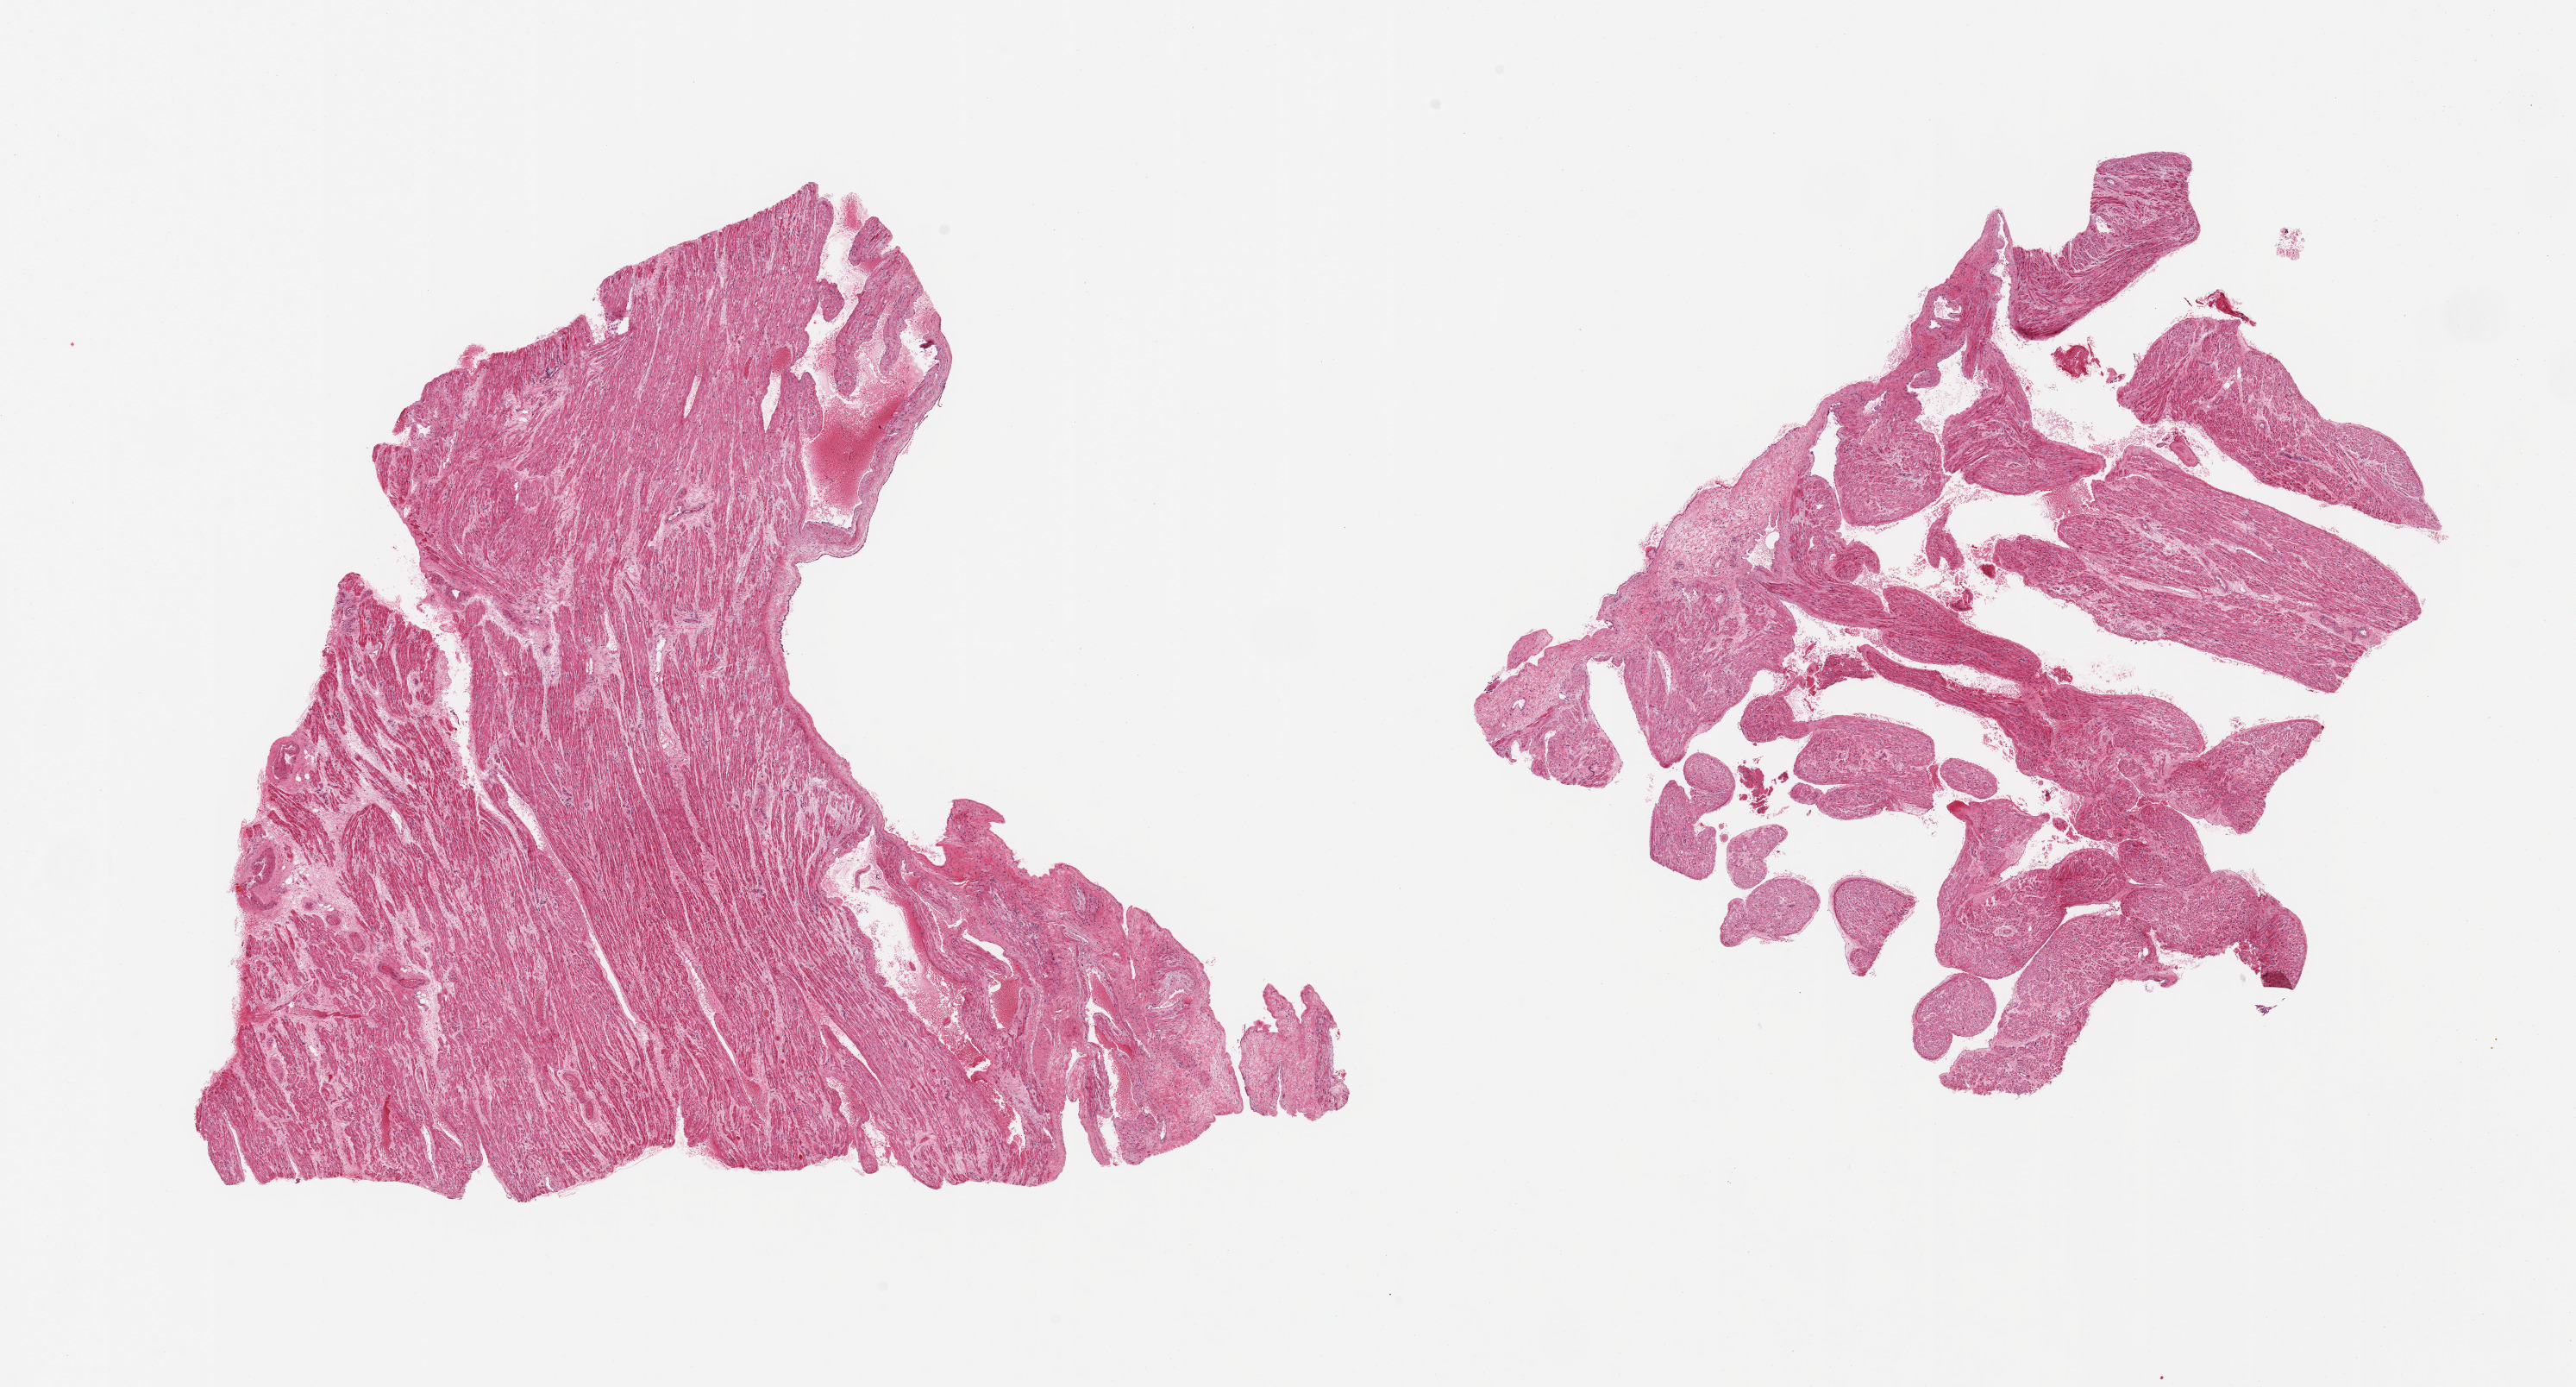
Digitized H&E-stained section, brightfield — a low-resolution overview of the entire scanned area, about 23.6 x 12.7 mm (from a 20x scan), PAXgene-fixed, paraffin-embedded tissue, sampled site (target tissue): auricular appendage, tissue donor sample. Donor: male.
Reviewer comment on this tissue sample: 2 pieces.